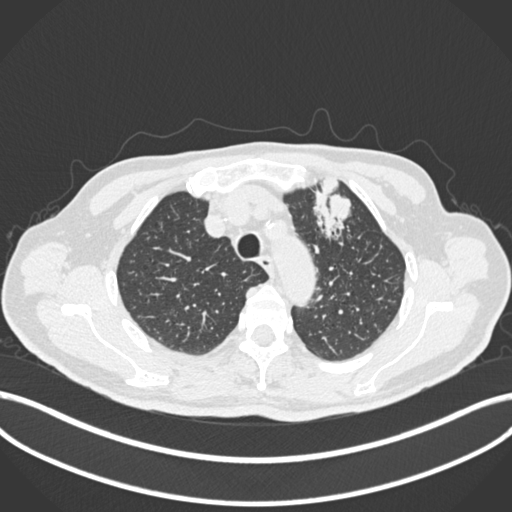
Chest CT, one axial slice; slice 205 of 261 in the series (ordered by position); 120 kVp; lung window (W 1500 / L -600 HU); 512 × 512 image matrix. Male patient, age 74 years. Case-level facts recorded for this patient, not image findings: clinical TNM (as recorded): T2b N0 M1c.
Annotated regions visible in this slice (rectangle marked by the reading radiologist):
- lung tumour (recorded histology: adenocarcinoma): box from (x=307, y=177) to (x=358, y=241) px